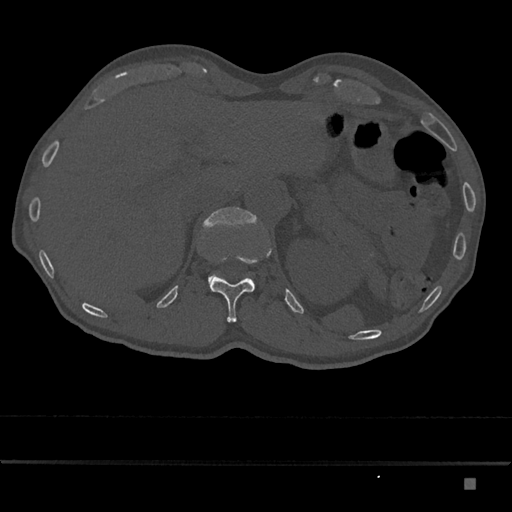
CT including the spine, one axial slice. Slice 594 of 797 in the series (ordered by position). 120 kVp. Bone window (W 1800 / L 400 HU). 0.5 mm slice thickness. 512 × 512 image matrix, field of view 390 × 390 mm. Male patient, age 72 years. Case-level facts recorded for this patient, not image findings: primary cancer: prostate.
Outlined on this slice (semi-automatic segmentation, software-assisted and operator-edited):
- L1 vertebra: bounding box [x1, y1, x2, y2] px = [203, 207, 257, 289]
- T12 vertebra: [210, 249, 271, 323]